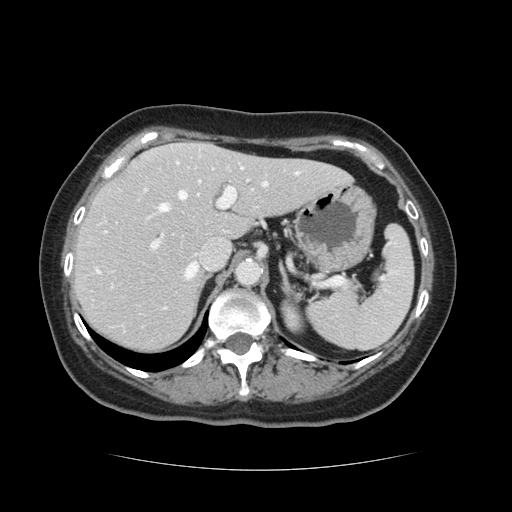
Contrast-enhanced abdominal CT, one axial slice. Slice 86 of 128 in the series (ordered by position). 120 kVp. Intravenous contrast given. Soft-tissue window (W 400 / L 40 HU). 2.5 mm slice thickness. 512 × 512 image matrix, field of view 366 × 366 mm. Female patient, age 67 years. Case-level facts recorded for this patient, not image findings: diagnosis: colorectal cancer liver metastases, imaged before liver resection; multiple liver metastases: yes; largest metastasis: 3 cm.
Outlined on this slice (outlined manually by an expert reader):
- hepatic veins: bounding box [x1, y1, x2, y2] px = [159, 173, 299, 279]
- liver: [74, 144, 348, 351]
- planned liver remnant (the part of the liver to remain after resection): [74, 157, 348, 351]
- portal vein (with intrahepatic branches): [153, 168, 249, 248]